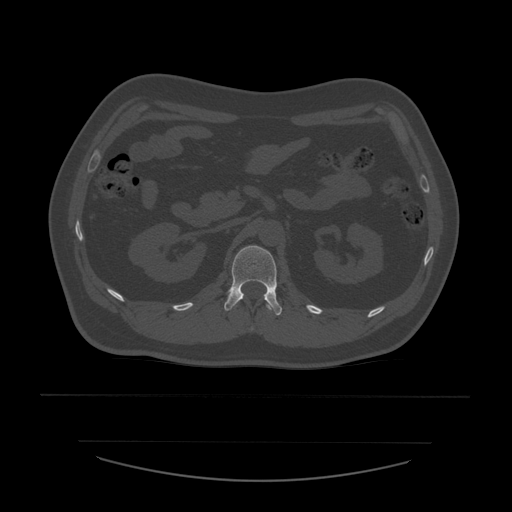
CT including the spine, one axial slice. Slice 232 of 532 in the series (ordered by position). Reconstruction kernel STANDARD. 120 kVp. Bone window (W 1800 / L 400 HU). 1.25 mm slice thickness. 512 × 512 image matrix, field of view 441 × 441 mm. Patient age 44 years. From the clinical record (not read from this slice): primary cancer: soft tissue sarcoma.
Outlined on this slice (semi-automatic segmentation, software-assisted and operator-edited):
- L1 vertebra: bounding box (x1, y1, x2, y2) in pixels: (224, 246, 282, 316)
- T12 vertebra: (251, 304, 272, 331)